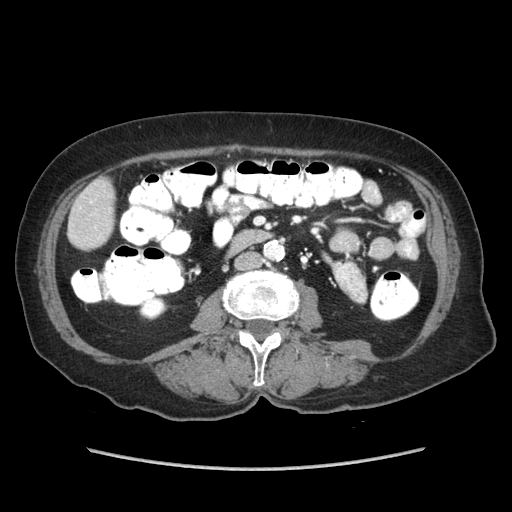
Contrast-enhanced abdominal CT (liver protocol), one axial slice. Slice 9 of 89 in the series (ordered by position). Reconstruction kernel STANDARD. Soft-tissue window (W 400 / L 40 HU). 2.5 mm slice thickness. 512 × 512 image matrix. From the clinical record (not read from this slice): diagnosis: hepatocellular carcinoma (patient treated with transarterial chemoembolisation; whether this scan precedes or follows treatment is not stated here); TNM stage (as recorded): Stage-IIIA; Child-Pugh class: A; tumour size: 11 cm.
Annotated regions visible in this slice (semi-automatically segmented with operator editing):
- liver parenchyma outside the tumour (the mass and vessels are separate outlines, so this box may not span the whole liver): bounding box (x1, y1, x2, y2) in pixels: (74, 178, 114, 224)